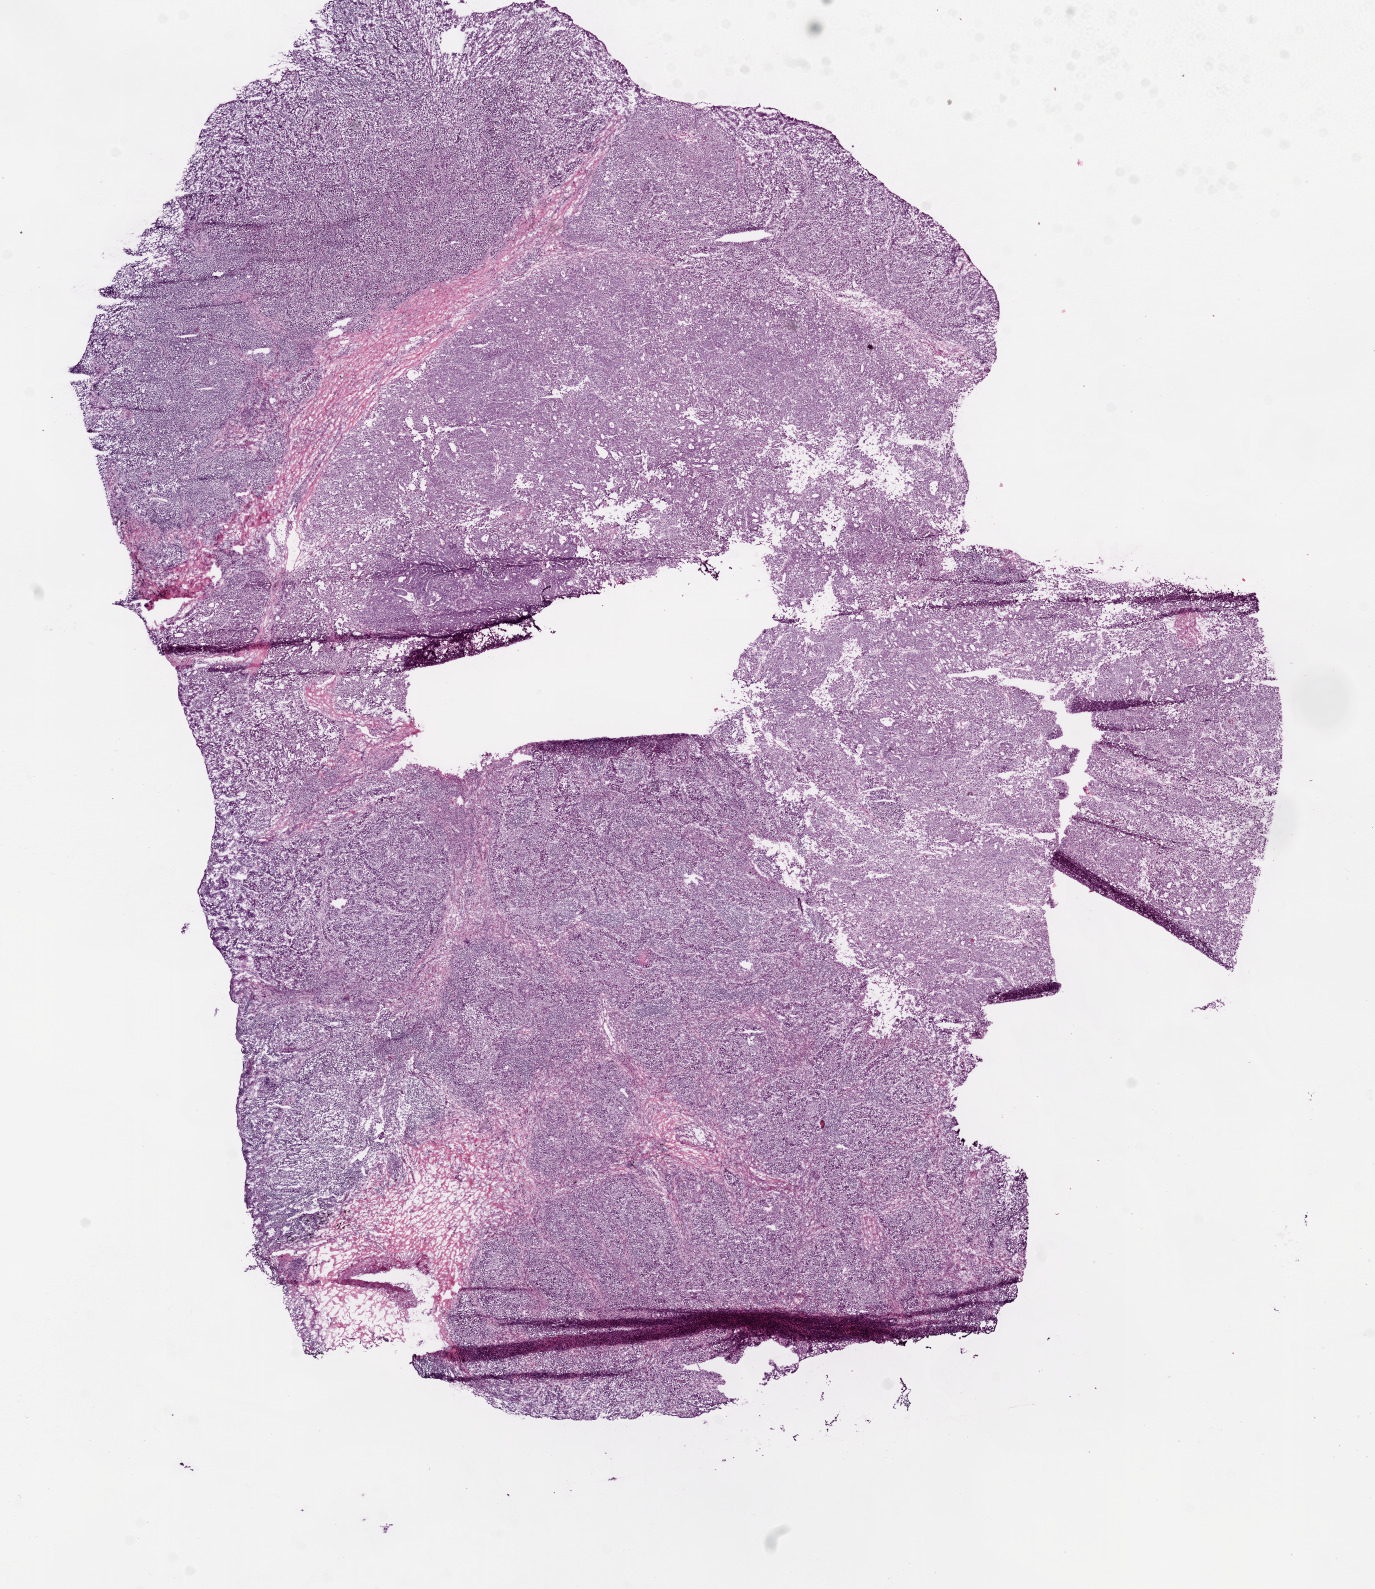
Whole-slide histology image, Hematoxylin and eosin (H&E) stained, low-resolution overview of the scanned area, about 11.0 x 12.8 mm; frozen section from the bottom of the tissue portion; sample: primary tumour, lung. Male, age 70 years at initial diagnosis. Composition of this section per pathologist review: tumour cells 82%, tumour nuclei 75%, normal cells 0%, stromal cells 15%, necrosis 3%.
* diagnosis: Adenocarcinoma with mixed subtypes
* laterality: right
* AJCC pathologic stage: IA